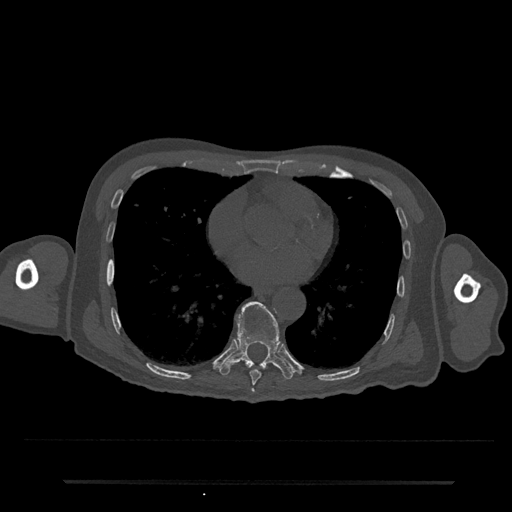
CT including the spine, one axial slice. Slice 388 of 797 in the series (ordered by position). Reconstruction kernel Br40s/3. Bone window (W 1800 / L 400 HU). 512 × 512 image matrix, field of view 427 × 427 mm. Patient: male, 74 years. From the clinical record (not read from this slice): primary cancer: prostate.
Structures marked on this image (semi-automatic segmentation, software-assisted and operator-edited):
- T7 vertebra: bounding box [x1, y1, x2, y2] px = [252, 389, 255, 393]
- T8 vertebra: [249, 370, 262, 386]
- T9 vertebra: [220, 301, 294, 380]